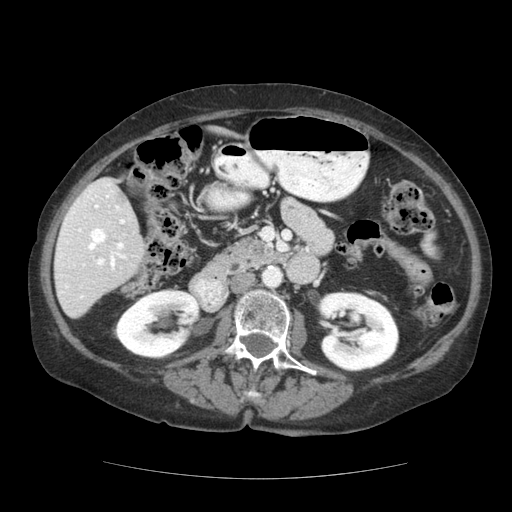
Contrast-enhanced abdominal CT (liver protocol), one axial slice; slice 55 of 111 in the series (ordered by position); reconstruction kernel STANDARD; 140 kVp; soft-tissue window (W 400 / L 40 HU); 2.5 mm slice thickness; 512 × 512 image matrix, field of view 360 × 360 mm. Case-level facts recorded for this patient, not image findings: diagnosis: hepatocellular carcinoma (patient treated with transarterial chemoembolisation; whether this scan precedes or follows treatment is not stated here); TNM stage (as recorded): Stage-I; Child-Pugh class: A; tumour differentiation: moderately-poorly differentiated; tumour nodularity: uninodular.
Annotated regions visible in this slice (semi-automatic segmentation, software-assisted and operator-edited):
- liver parenchyma outside the tumour (the mass and vessels are separate outlines, so this box may not span the whole liver): bounding box (x1, y1, x2, y2) in pixels: (54, 130, 231, 318)
- liver vessels: (58, 184, 126, 298)